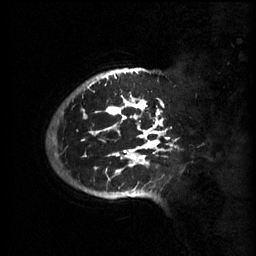
Breast MRI (dynamic contrast-enhanced), one sagittal slice; slice 49 of 60 in the series (ordered by position); 3 images stored at this slice position (order not interpretable as contrast timing); 1.5 T; TE 4.2 ms, TR 11 ms; 2 mm slice thickness; 256 × 256 image matrix. Female patient, age 51 years.
Annotated regions visible in this slice (semi-automatic segmentation, software-assisted and operator-edited):
- analysis volume of interest (the breast-tissue region the enhancement analysis was run in; not a lesion): bounding box [x1, y1, x2, y2] px = [64, 80, 183, 201]
- tumour enhancement mask (voxels above the 70 % enhancement threshold inside the analysis volume of interest): [81, 80, 173, 197]